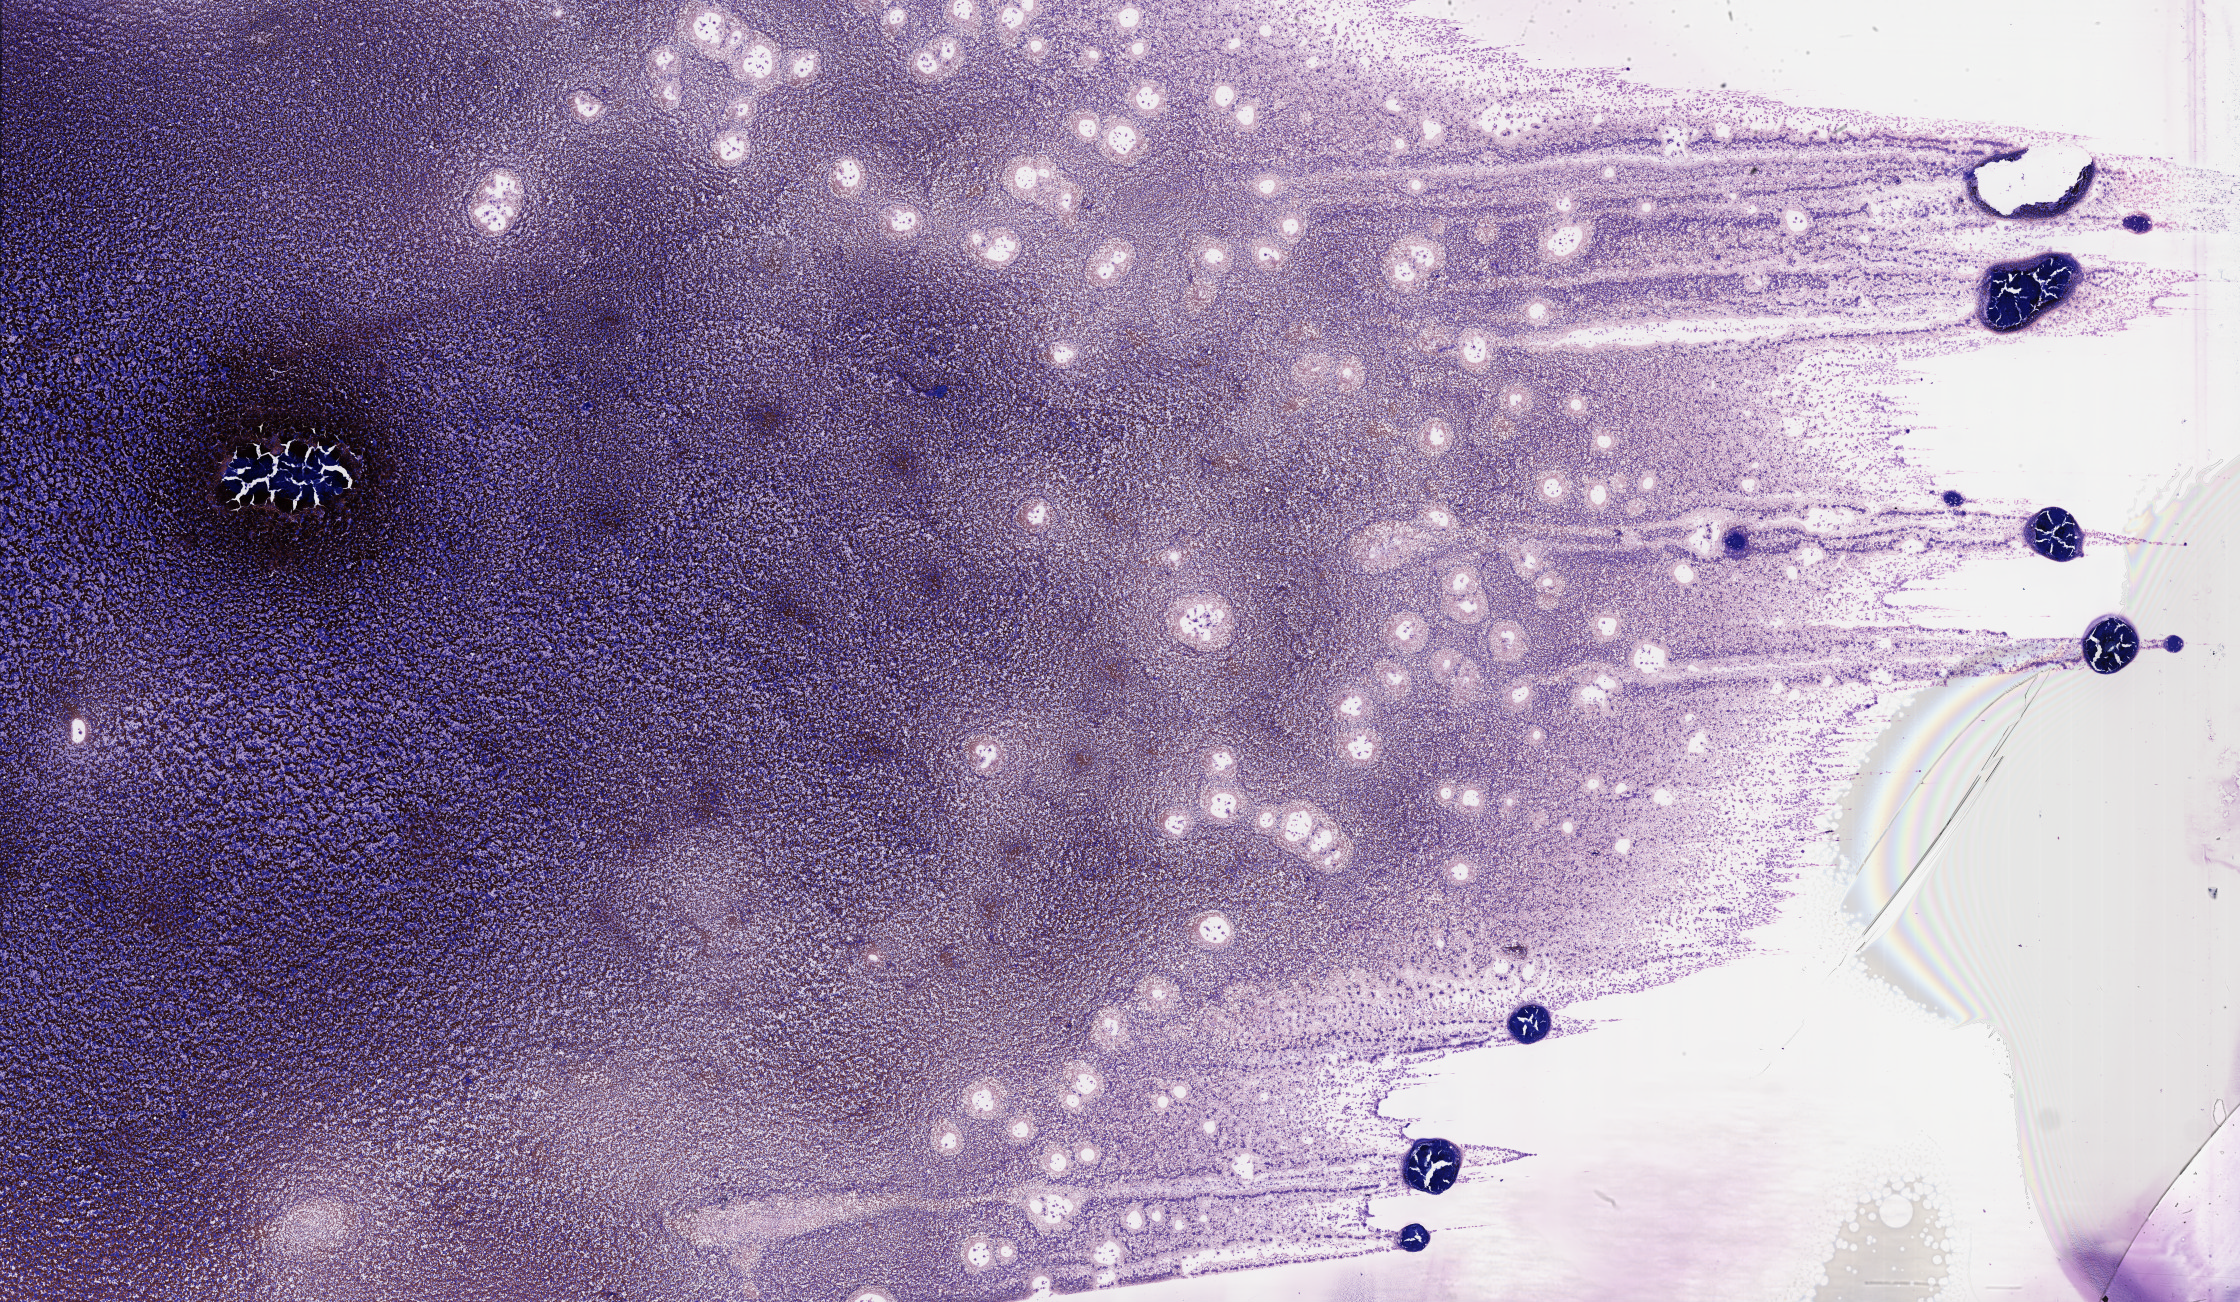
Digitized Wright-Giemsa-stained section, low-resolution overview of the scanned area, about 36.2 x 21.1 mm, frozen section (tissue freezing medium), primary tumor, site: bone marrow. Male patient, 18 years old. Composition of this section per pathologist review: tumor cells 80%, tumor nuclei 80%, stromal cells 5%, necrosis 0%, normal cells 15%. Inflammatory infiltration, as recorded: lymphocyte infiltration 15%, monocyte infiltration 40%, neutrophil infiltration 40%.
- Ann Arbor stage (patient): Stage IV
- histologic diagnosis: Burkitt lymphoma, NOS